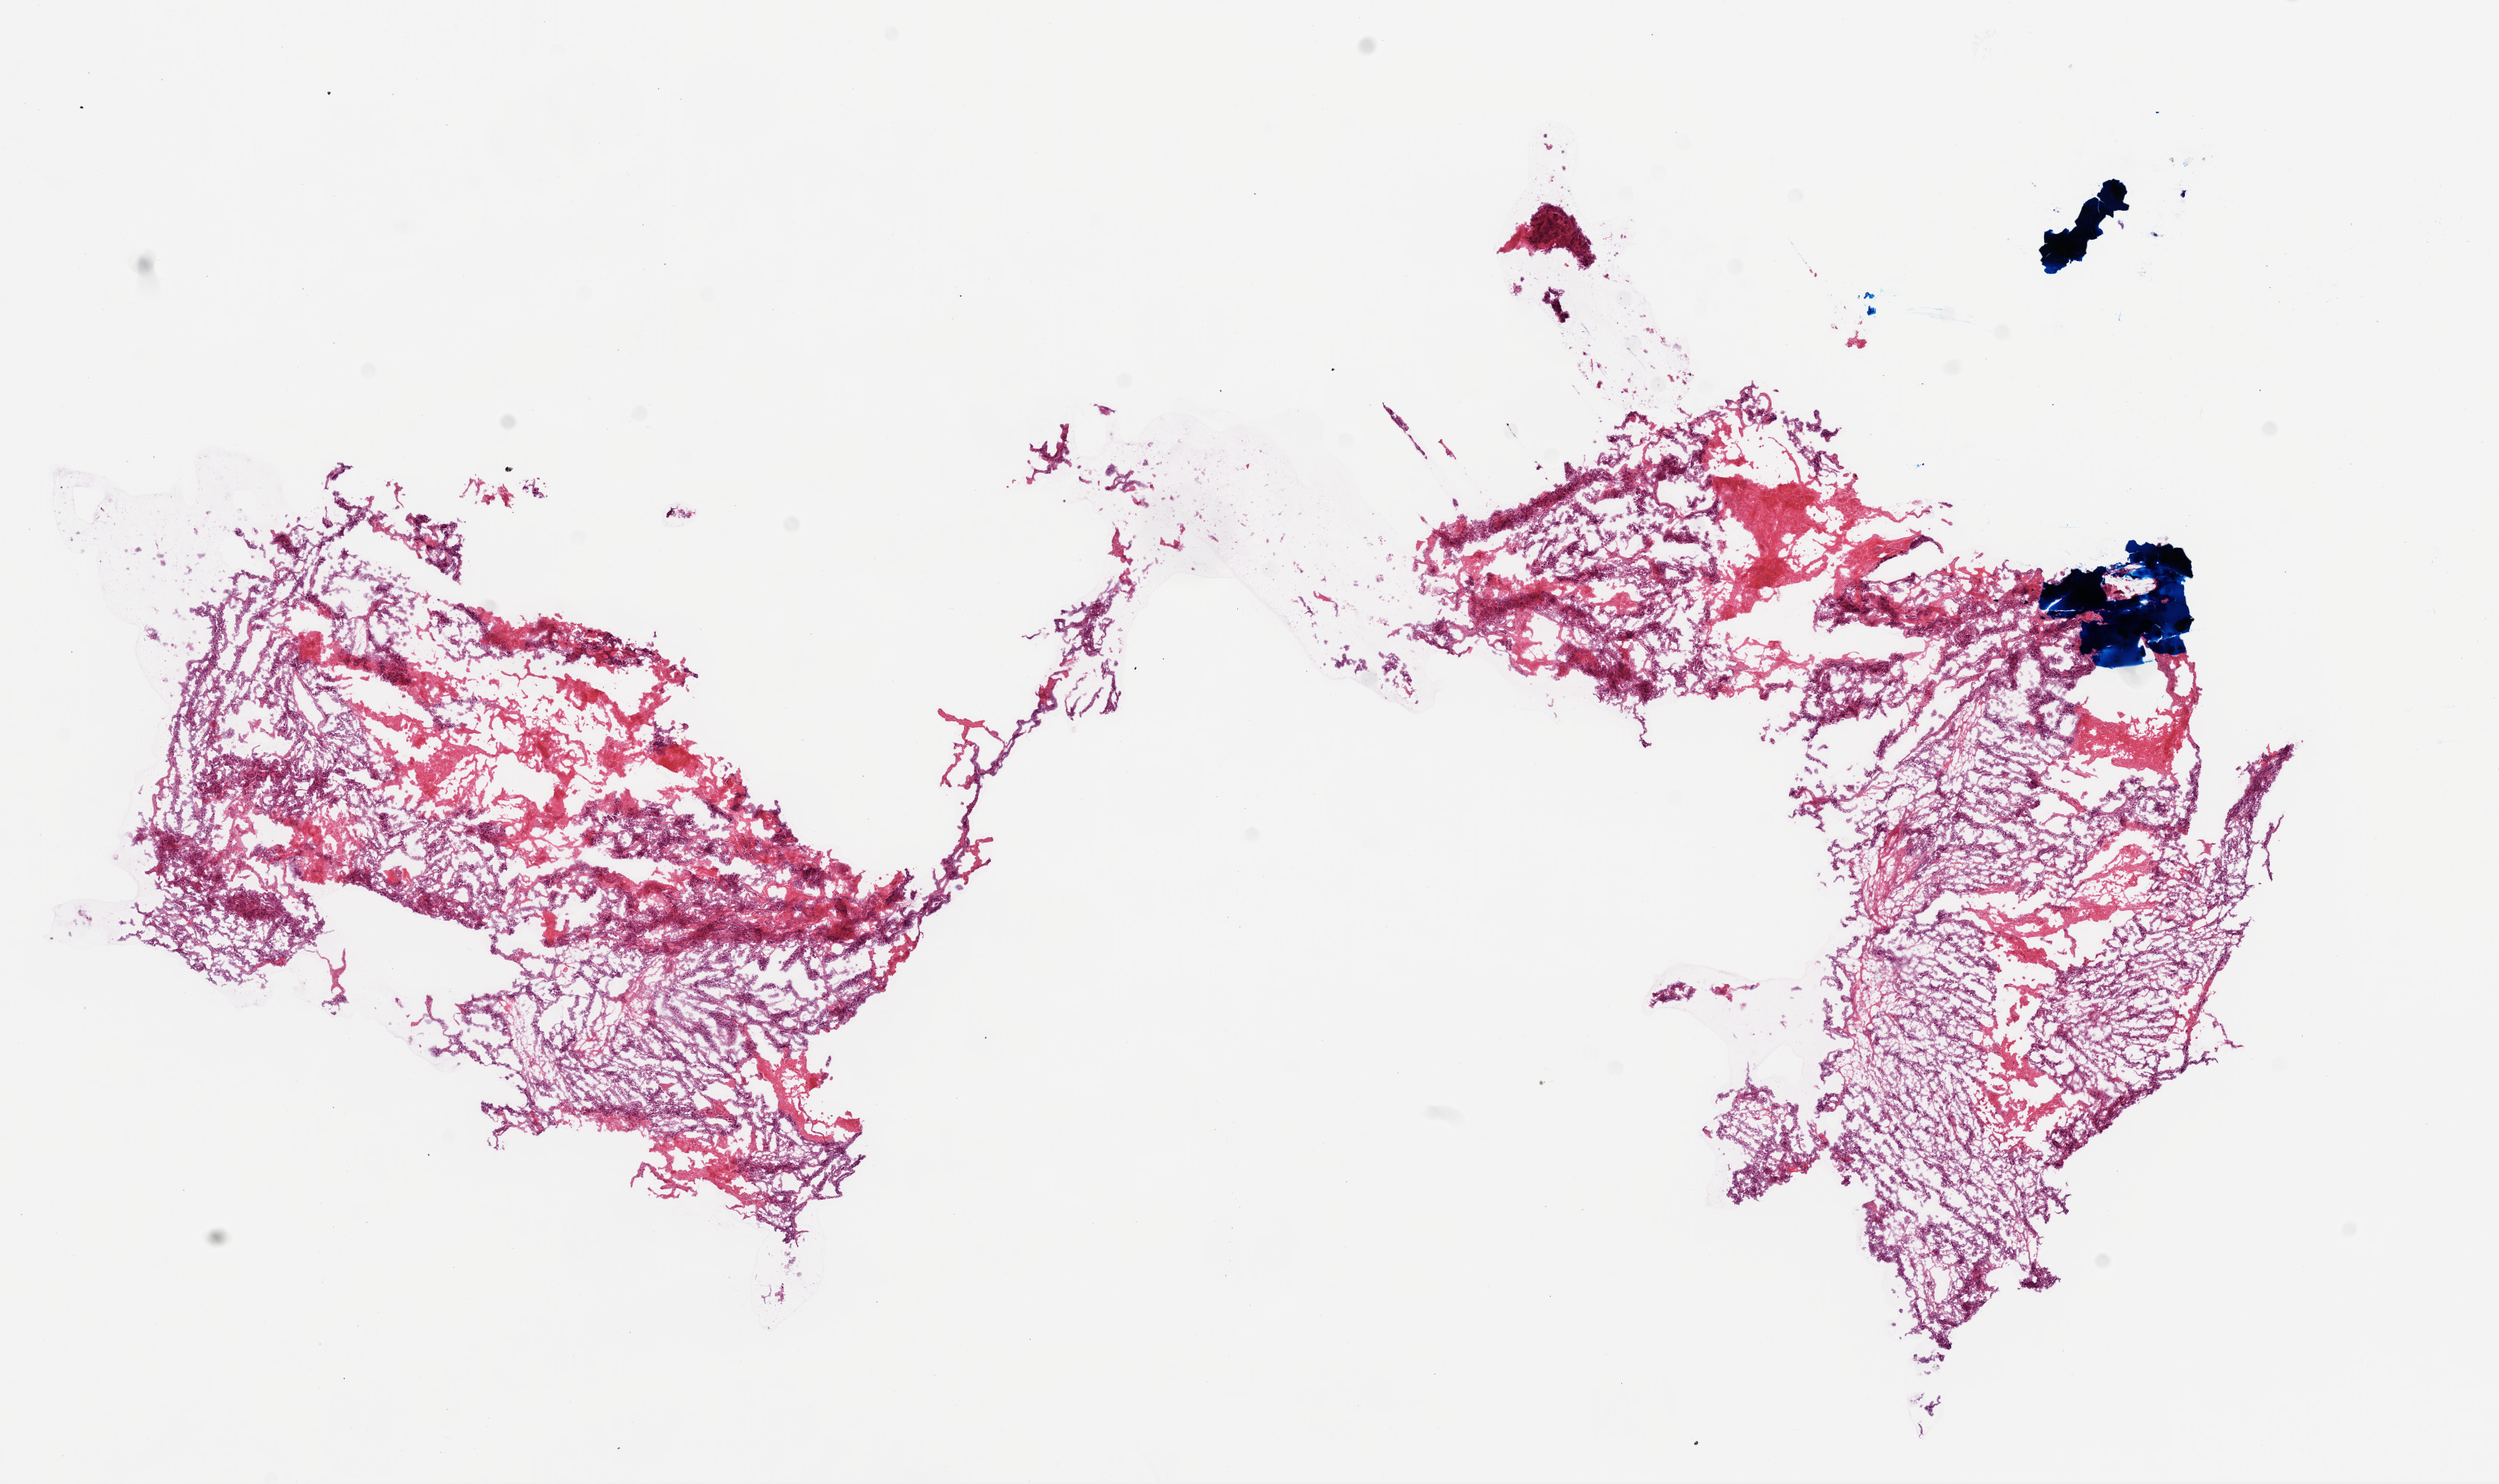
Whole-slide histology image, Hematoxylin and eosin (H&E) stained, low-resolution overview of the scanned area, about 13.5 x 8.0 mm (acquisition: 20x scan); frozen section from the top of the tissue portion; ovary, primary tumour sample. Female patient; age at initial diagnosis 60 years. Histologic grade: G3 (poorly differentiated). Composition of this section per pathologist review: tumour cells 85%, tumour nuclei 90%, normal cells 10%, stromal cells 5%, necrosis 0%.
Pathologic diagnosis: Serous cystadenocarcinoma, NOS. FIGO stage: IV. Laterality: left.